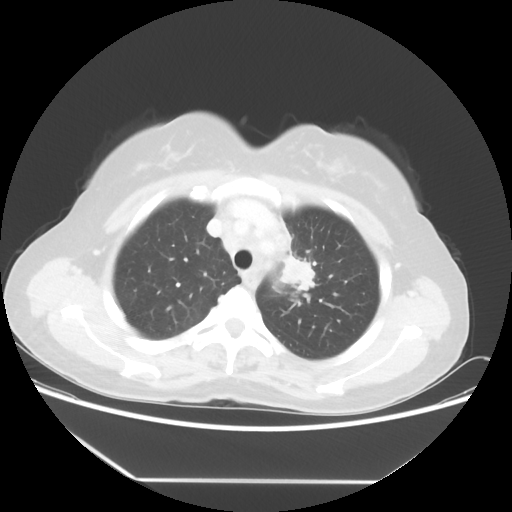
Chest CT, one axial slice; position 41 of 52 along the scan axis; reconstruction kernel STANDARD; lung window (W 1500 / L -600 HU); 5 mm slice thickness; 512 × 512 image matrix, field of view 390 × 390 mm. Female patient, age 50 years. From the clinical record (not read from this slice): clinical TNM (as recorded): T2 N3 M0.
Structures marked on this image (rectangle marked by the reading radiologist):
- lung tumour (recorded histology: adenocarcinoma): bounding box <267,242,329,298> (left, top, right, bottom; pixels)